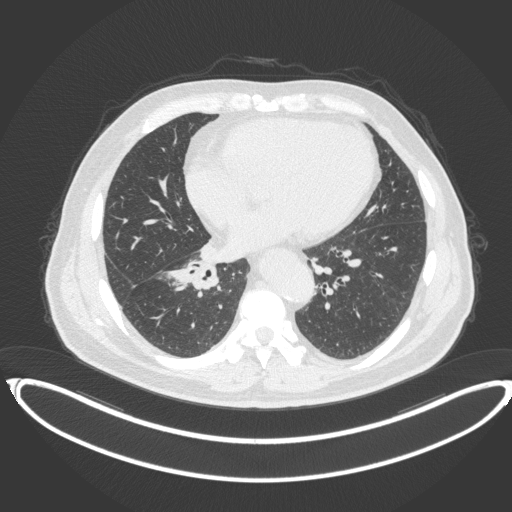
Chest CT, one axial slice; 120 kVp; lung window (W 1500 / L -600 HU); 1 mm slice thickness; 512 × 512 image matrix, field of view 448 × 448 mm. Male patient, age 61 years. Case-level facts recorded for this patient, not image findings: clinical TNM (as recorded): T1b N1 M0.
Structures marked on this image (bounding box drawn by a radiologist):
- lung tumour (recorded histology: squamous cell carcinoma): bounding box <183,259,220,293> (left, top, right, bottom; pixels)